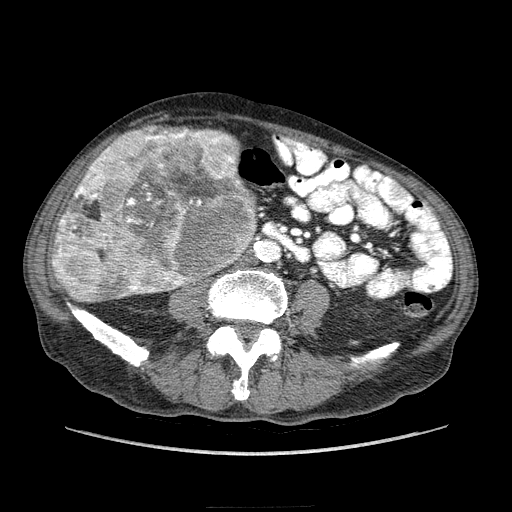
Contrast-enhanced abdominal CT (liver protocol), one axial slice; position 51 of 218 along the scan axis; 100 kVp; soft-tissue window (W 400 / L 40 HU); 2.5 mm slice thickness; 512 × 512 image matrix, field of view 380 × 380 mm. From the clinical record (not read from this slice): diagnosis: hepatocellular carcinoma (patient treated with transarterial chemoembolisation; whether this scan precedes or follows treatment is not stated here); TNM stage (as recorded): Stage-IIIA; Child-Pugh class: A; tumour differentiation: well differentiated; tumour nodularity: multinodular.
Structures marked on this image (semi-automatically segmented with operator editing):
- liver parenchyma outside the tumour (the mass and vessels are separate outlines, so this box may not span the whole liver): bounding box [x1, y1, x2, y2] px = [53, 171, 256, 276]
- mass: [51, 125, 257, 303]